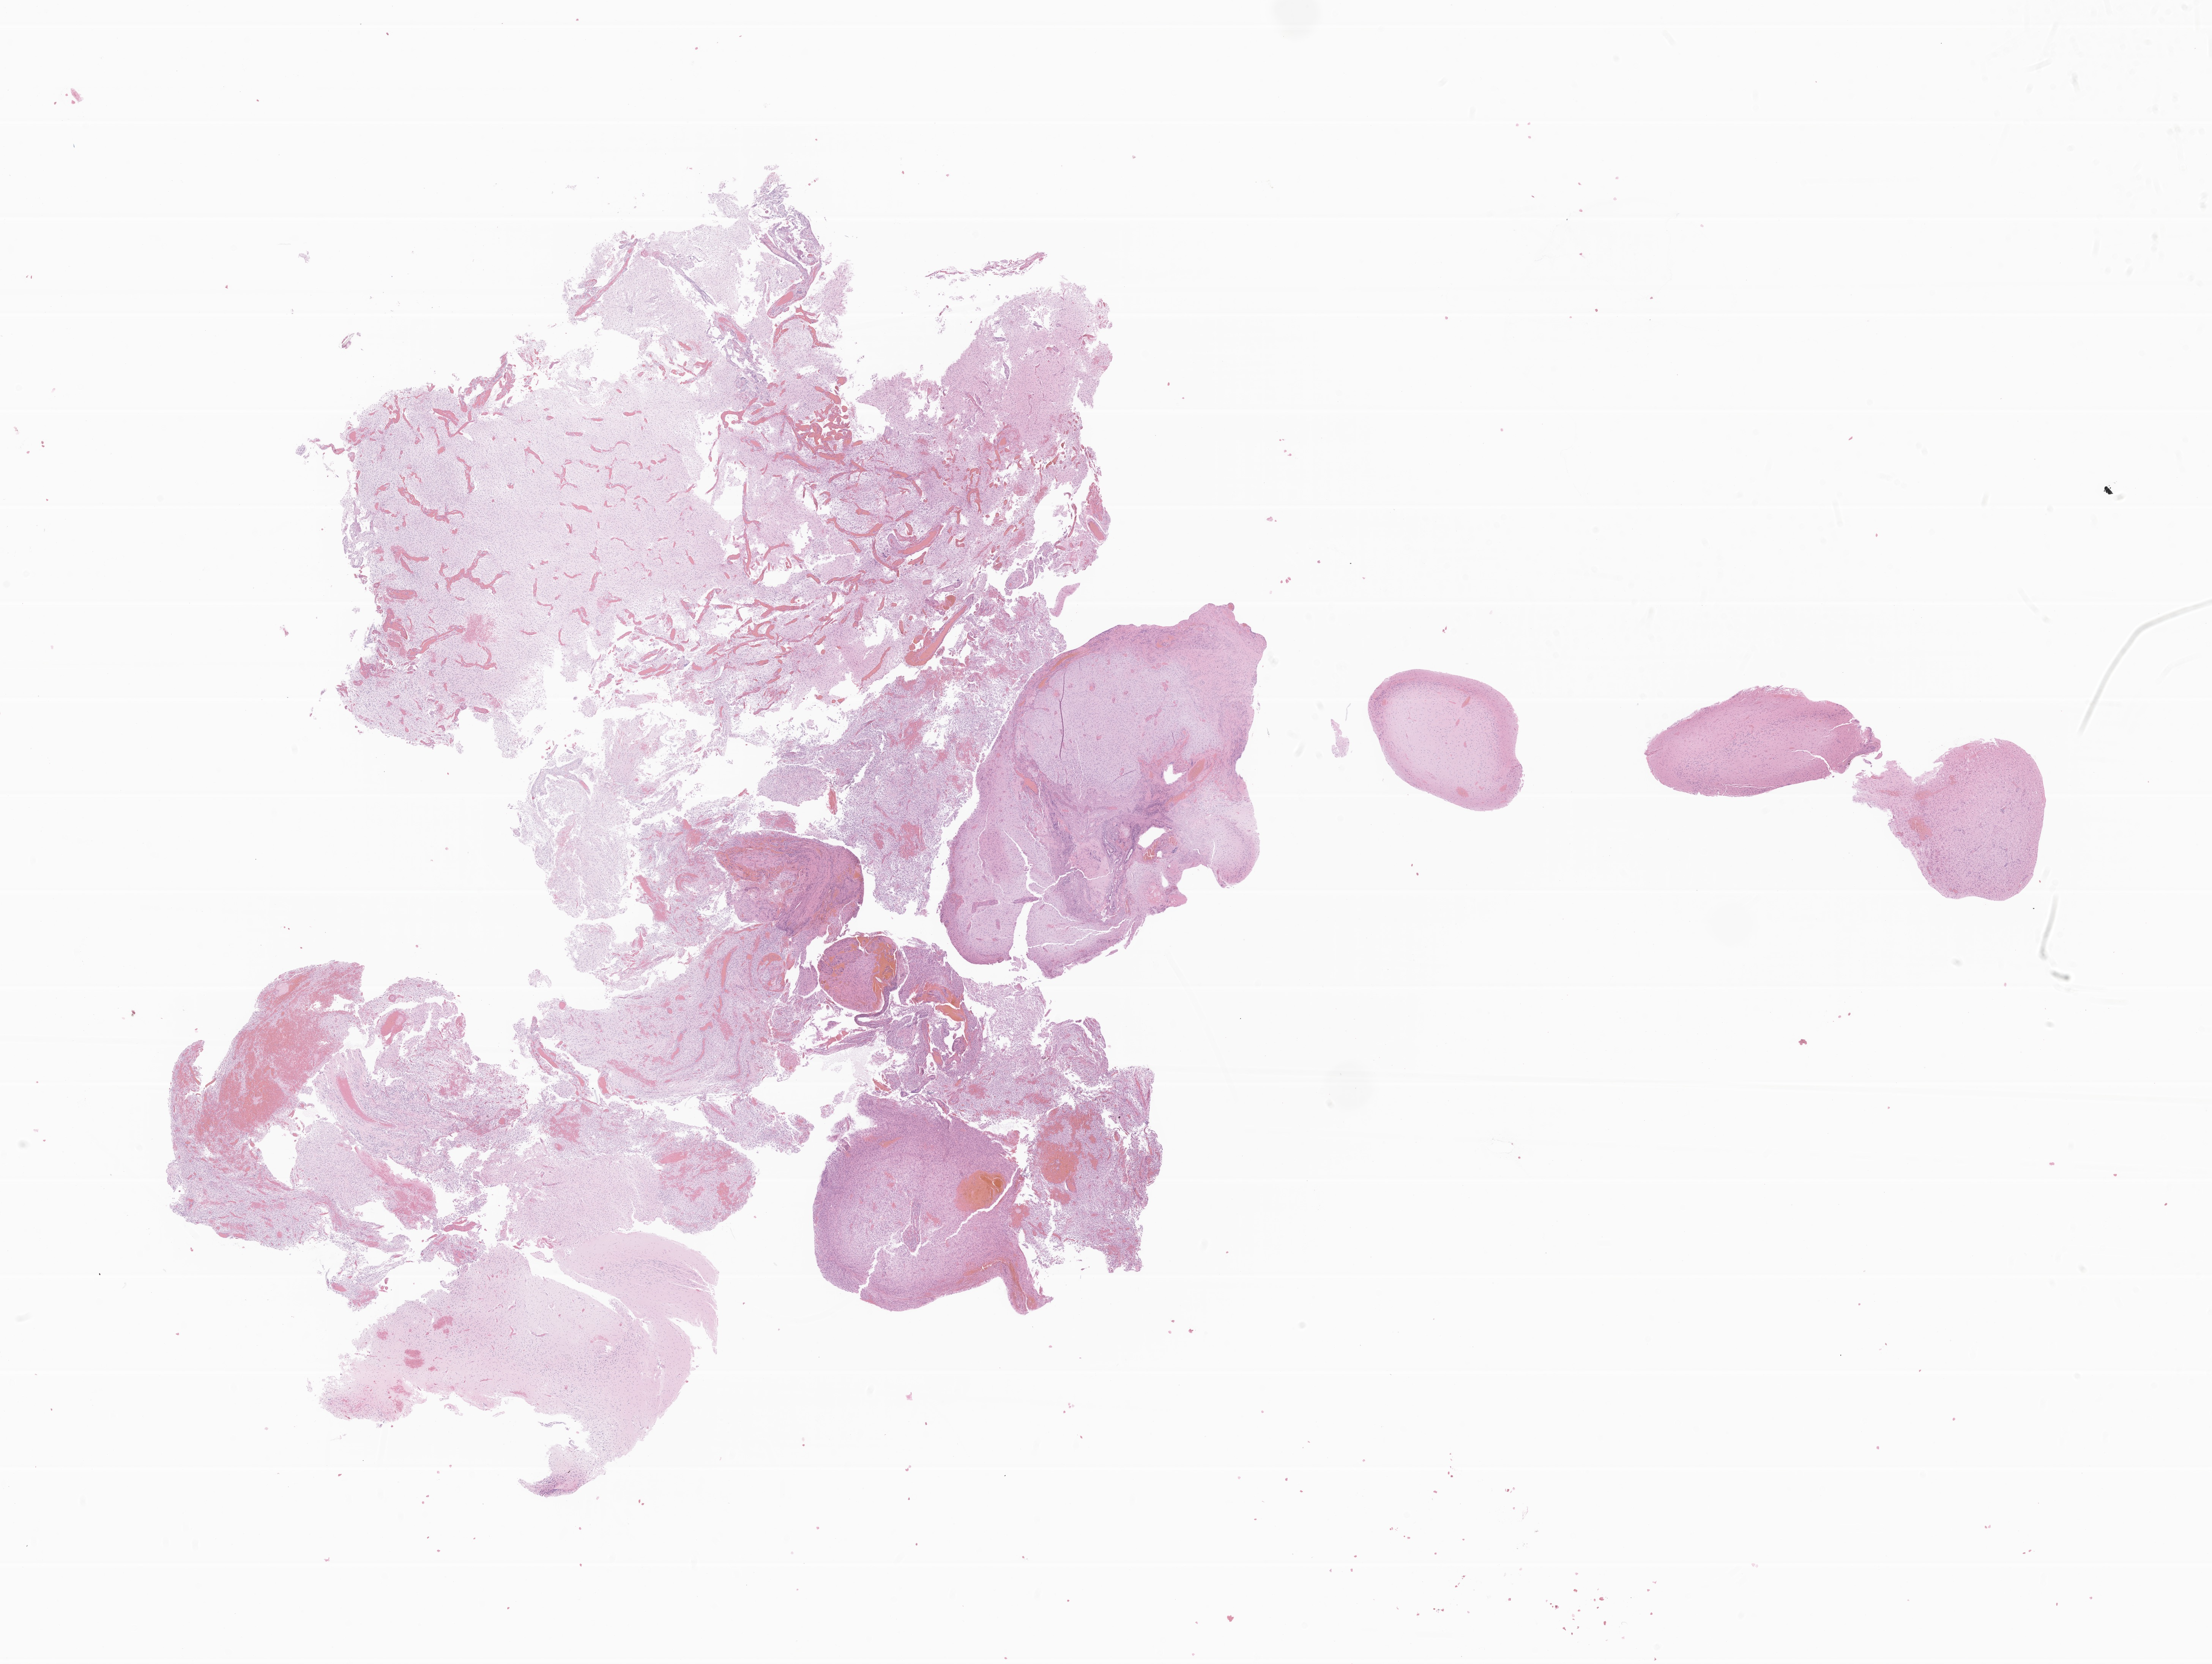
Whole-slide image, H&E stain of tumor tissue from the cerebellum — low-resolution overview of the scanned area, about 24.6 x 18.5 mm, formalin-fixed, paraffin-embedded (FFPE) tissue. Patient female; age 47 months (3 years 11 months).
Diagnosis: Pilocytic astrocytoma.